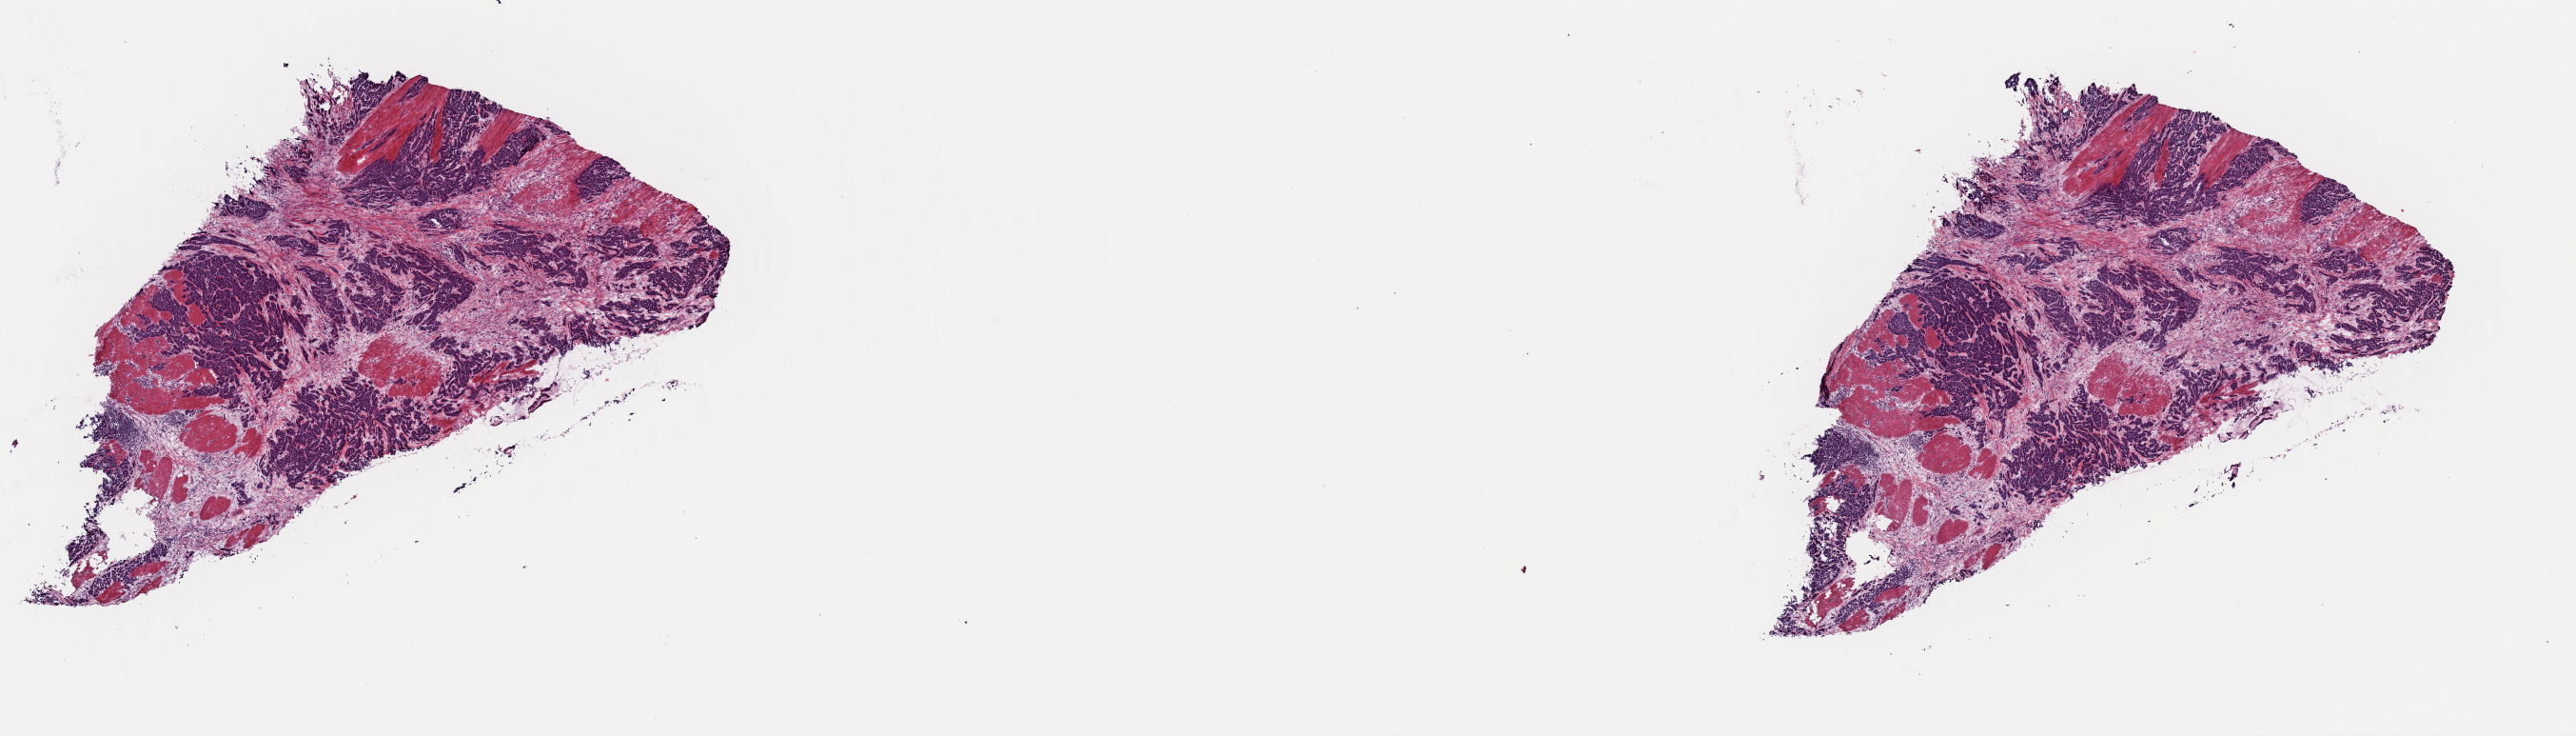
Digitized Hematoxylin and eosin (H&E) stained tissue section (whole slide), low-resolution overview of the scanned area, about 21.4 x 6.1 mm (slide scanned at 40x). Frozen section from the top of the tissue portion. Sample: primary tumour, stomach. Female, age 72 years at initial diagnosis. Histologic grade: G3 (poorly differentiated). Slide review estimates, as recorded: tumour cells 50%, tumour nuclei 60%, normal cells 10%, stromal cells 40%, necrosis 0%. Infiltration values recorded for this section: lymphocyte infiltration 0%, monocyte infiltration 0%, neutrophil infiltration 0%.
Histologic diagnosis: Tubular adenocarcinoma (gastric antrum). AJCC pathologic stage: IIIA.